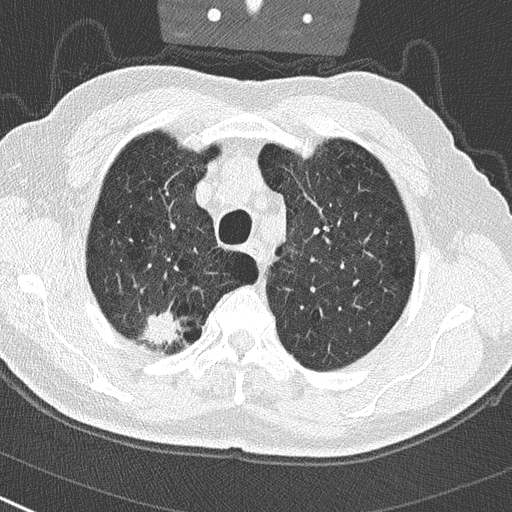
Low-dose screening chest CT, one axial slice. Position 235 of 290 along the scan axis. 120 kVp. Lung window (W 1500 / L -600 HU). 2 mm slice thickness. 512 × 512 image matrix.
Outlined on this slice (expert manual segmentation):
- lesion 1 (tumor, upper lobe of right lung): bounding box (x1, y1, x2, y2) in pixels: (137, 312, 180, 345)